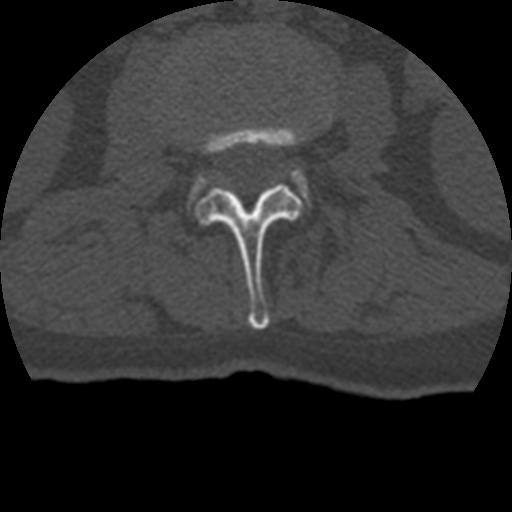
CT including the spine, one axial slice. Position 108 of 399 along the scan axis. Reconstruction kernel STANDARD. Bone window (W 1800 / L 400 HU). 1.25 mm slice thickness. 512 × 512 image matrix, field of view 160 × 160 mm. Patient age 69 years. From the clinical record (not read from this slice): primary cancer: prostate.
Annotated regions visible in this slice (semi-automatically segmented with operator editing):
- L2 vertebra: box from (x=195, y=124) to (x=305, y=329) px
- L3 vertebra: (x=194, y=169)–(x=309, y=198)